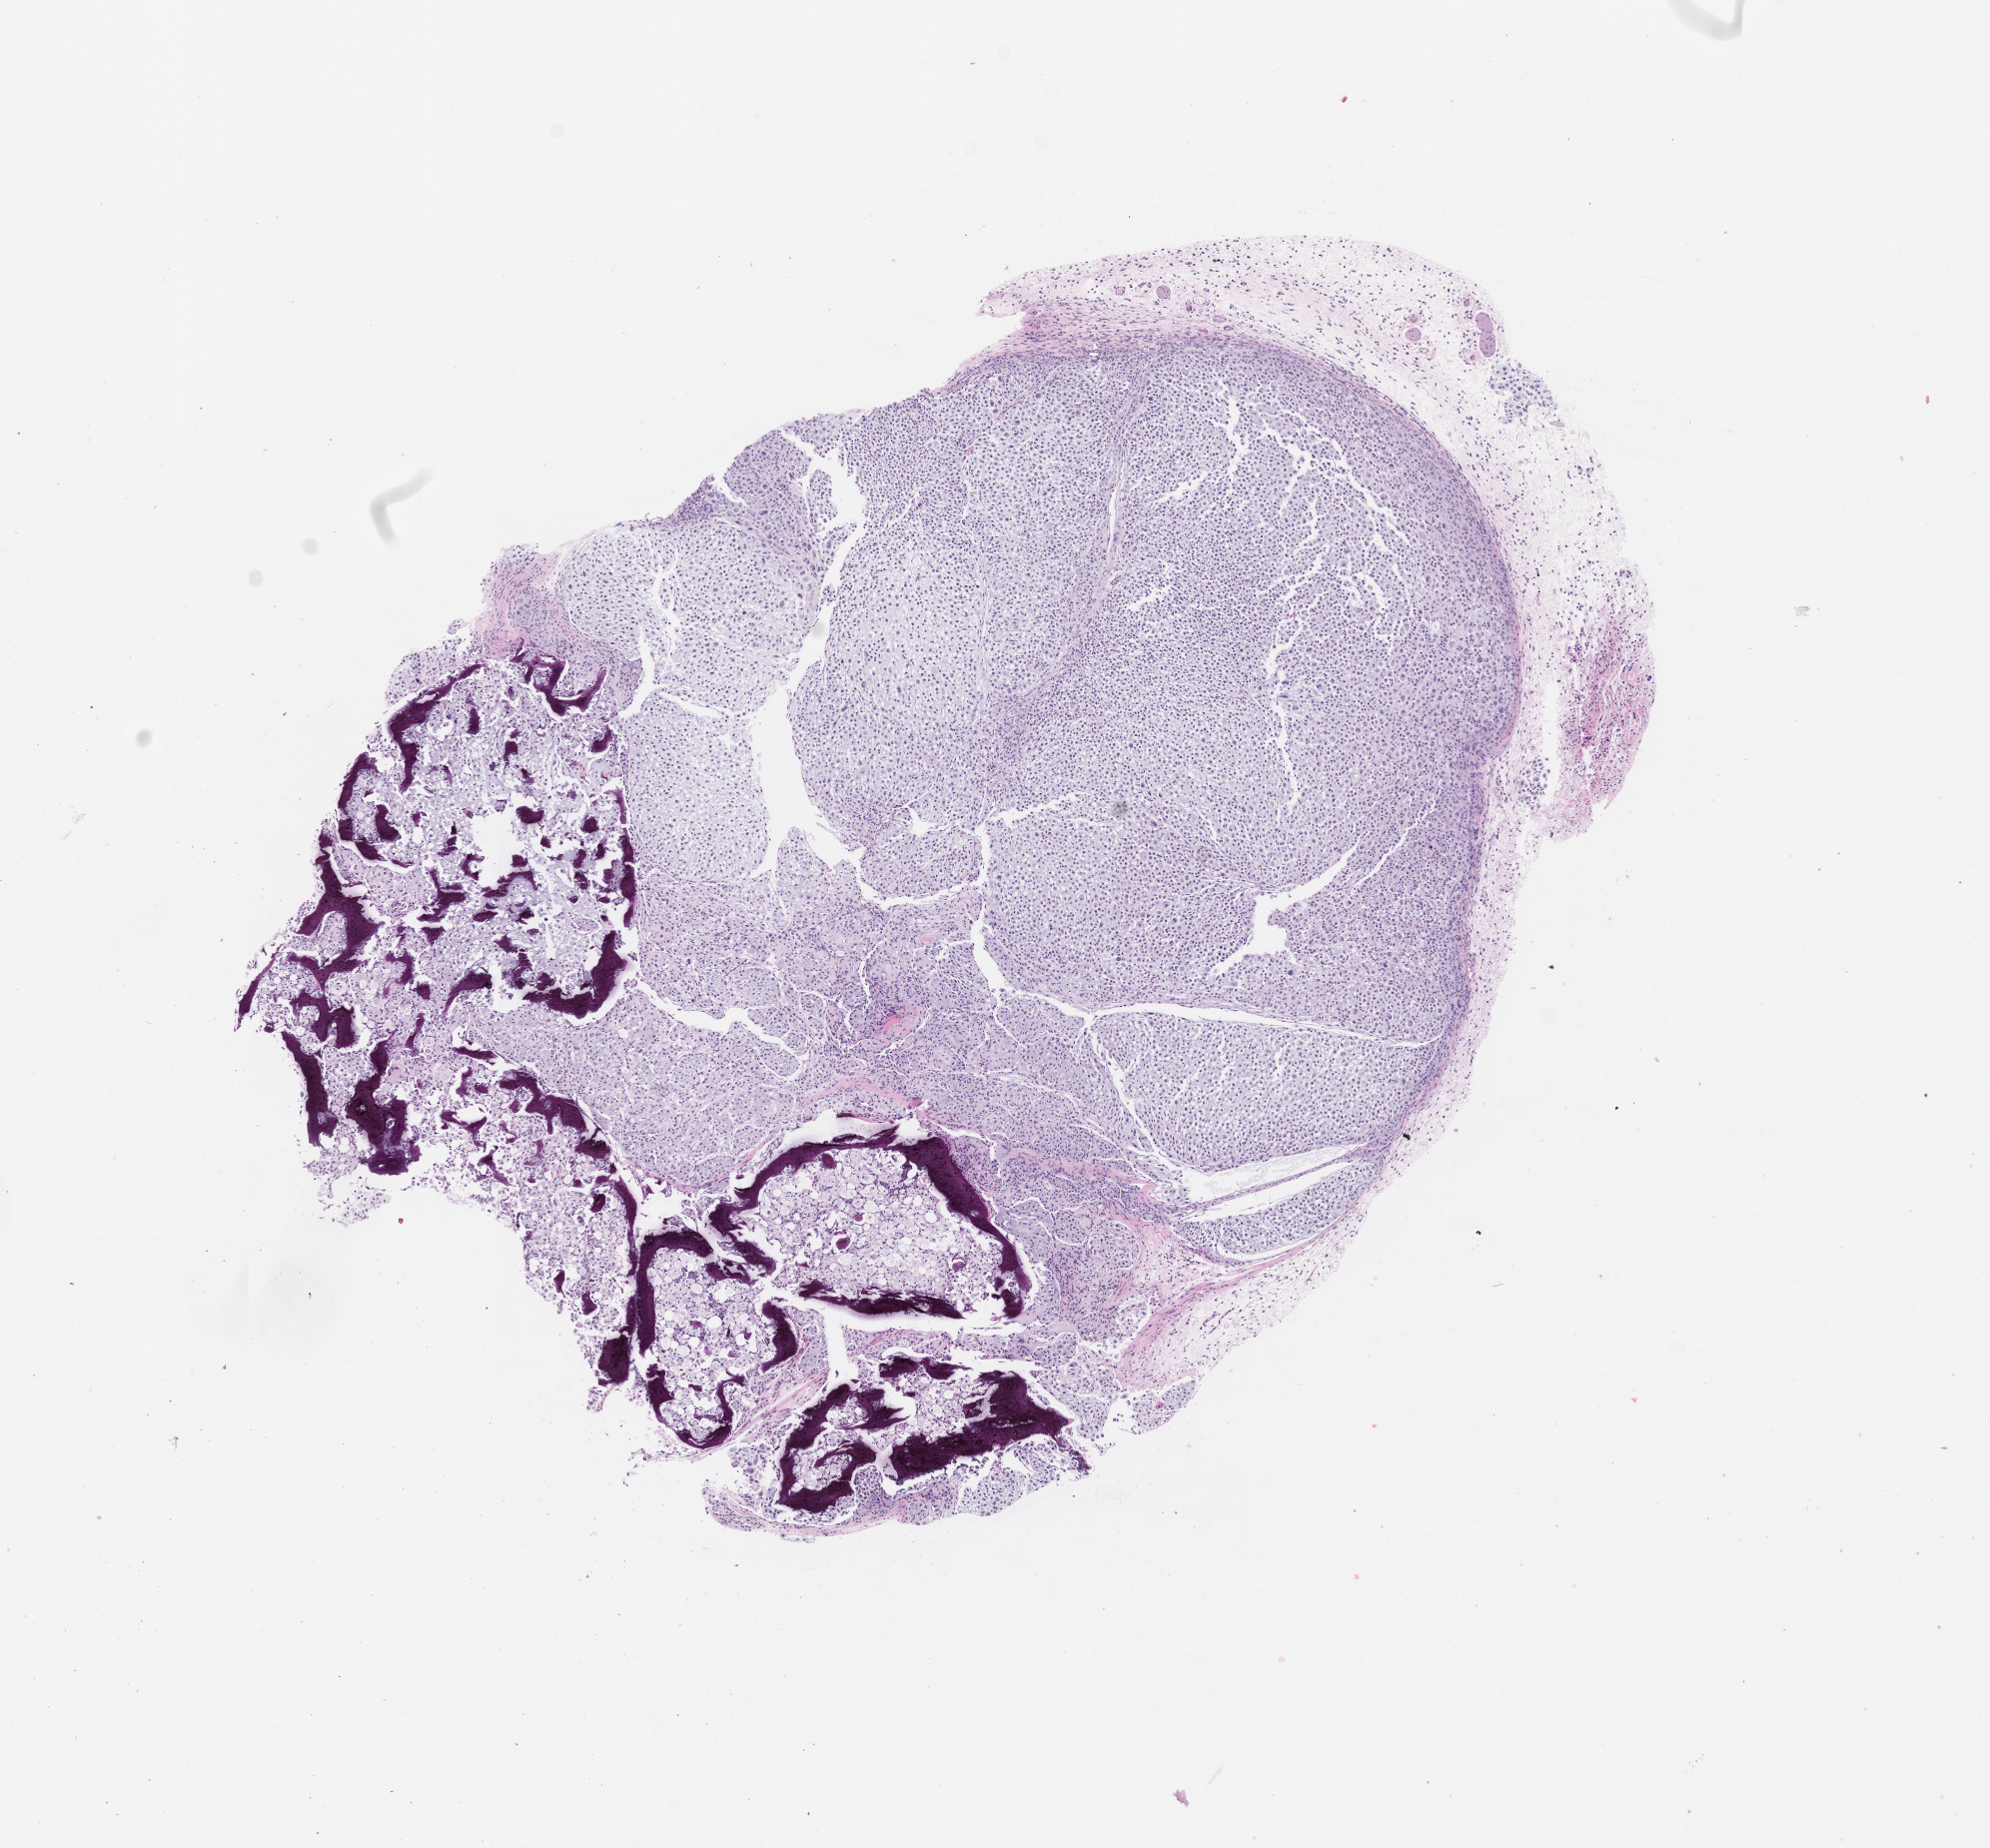
Whole-slide image, hematoxylin and eosin (H&E): patient-derived xenograft (human tumor grown in a mouse), passage 2, shown as a low-resolution overview of the whole scanned area (about 8.0 x 7.4 mm). Formalin-fixed paraffin-embedded section. Originating tumor site category: musculoskeletal.
Originating patient diagnosis: Chondrosarcoma.